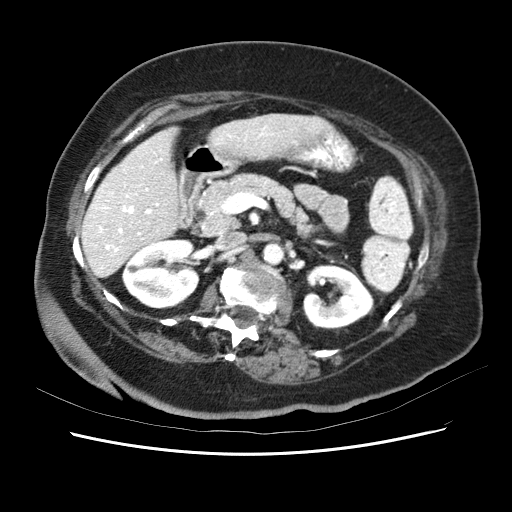
Contrast-enhanced abdominal CT (liver protocol), one axial slice; slice 23 of 62 in the series (ordered by position); reconstruction kernel STANDARD; 120 kVp; soft-tissue window (W 400 / L 40 HU); 2.5 mm slice thickness; 512 × 512 image matrix. Case-level facts recorded for this patient, not image findings: diagnosis: hepatocellular carcinoma (patient treated with transarterial chemoembolisation; whether this scan precedes or follows treatment is not stated here); TNM stage (as recorded): Stage-I; Child-Pugh class: B; tumour nodularity: uninodular.
Structures marked on this image (semi-automatic segmentation, software-assisted and operator-edited):
- liver parenchyma outside the tumour (the mass and vessels are separate outlines, so this box may not span the whole liver): bounding box [x1, y1, x2, y2] px = [82, 112, 342, 278]
- liver vessels: [85, 120, 266, 266]